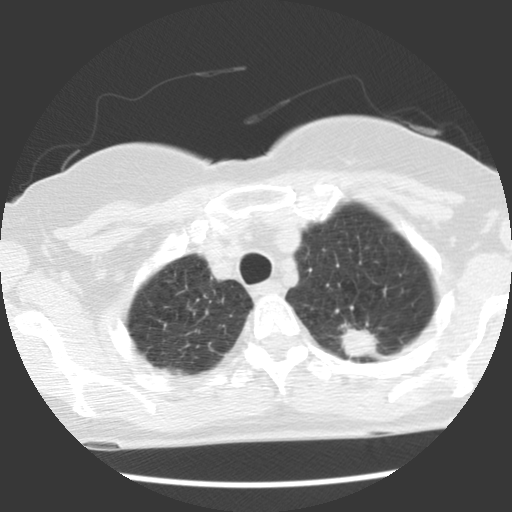
Low-dose screening chest CT, one axial slice. Position 99 of 120 along the scan axis. Reconstruction kernel STANDARD. Lung window (W 1500 / L -600 HU). 2.5 mm slice thickness. 512 × 512 image matrix, field of view 300 × 300 mm.
Structures marked on this image (expert manual segmentation):
- lesion 1 (tumor, upper lobe of left lung): bounding box [x1, y1, x2, y2] px = [341, 324, 378, 357]